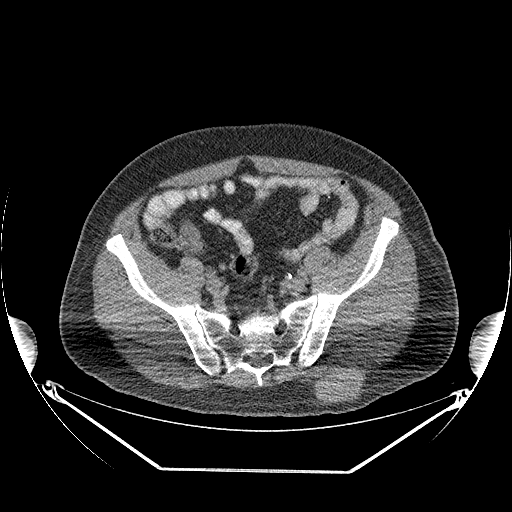
CT of an extremity soft-tissue mass (from a PET/CT study), one axial slice; slice 84 of 267 in the series (ordered by position); reconstruction kernel STANDARD; soft-tissue window (W 400 / L 40 HU); 512 × 512 image matrix, field of view 500 × 500 mm. Male patient. Case-level facts recorded for this patient, not image findings: histological type: pleiomorphic leiomyosarcoma; grade: high; site of the primary tumour: left buttock.
Annotated regions visible in this slice (expert contour drawn on MRI and transferred to this co-registered scan by the dataset authors):
- gross tumour volume including surrounding oedema: bounding box [x1, y1, x2, y2] px = [313, 370, 366, 403]
- gross tumour volume (mass): [317, 372, 364, 403]